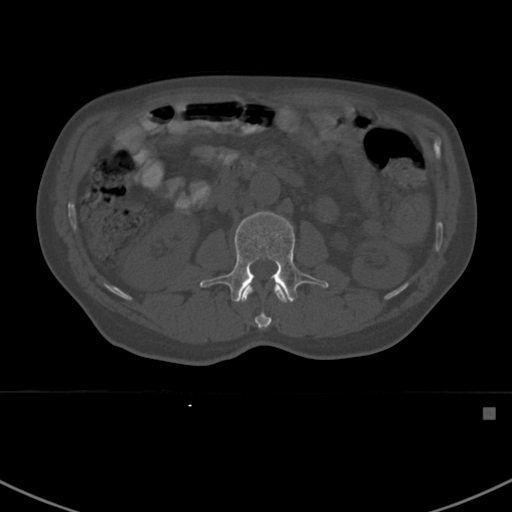
CT including the spine, one axial slice. Slice 291 of 412 in the series (ordered by position). Reconstruction kernel Br40s. Bone window (W 1800 / L 400 HU). 512 × 512 image matrix, field of view 358 × 358 mm. Male patient, age 59 years. From the clinical record (not read from this slice): primary cancer: prostate.
Annotated regions visible in this slice (semi-automatically segmented with operator editing):
- L1 vertebra: bounding box <242,285,287,329> (left, top, right, bottom; pixels)
- L2 vertebra: <200,211,329,303>